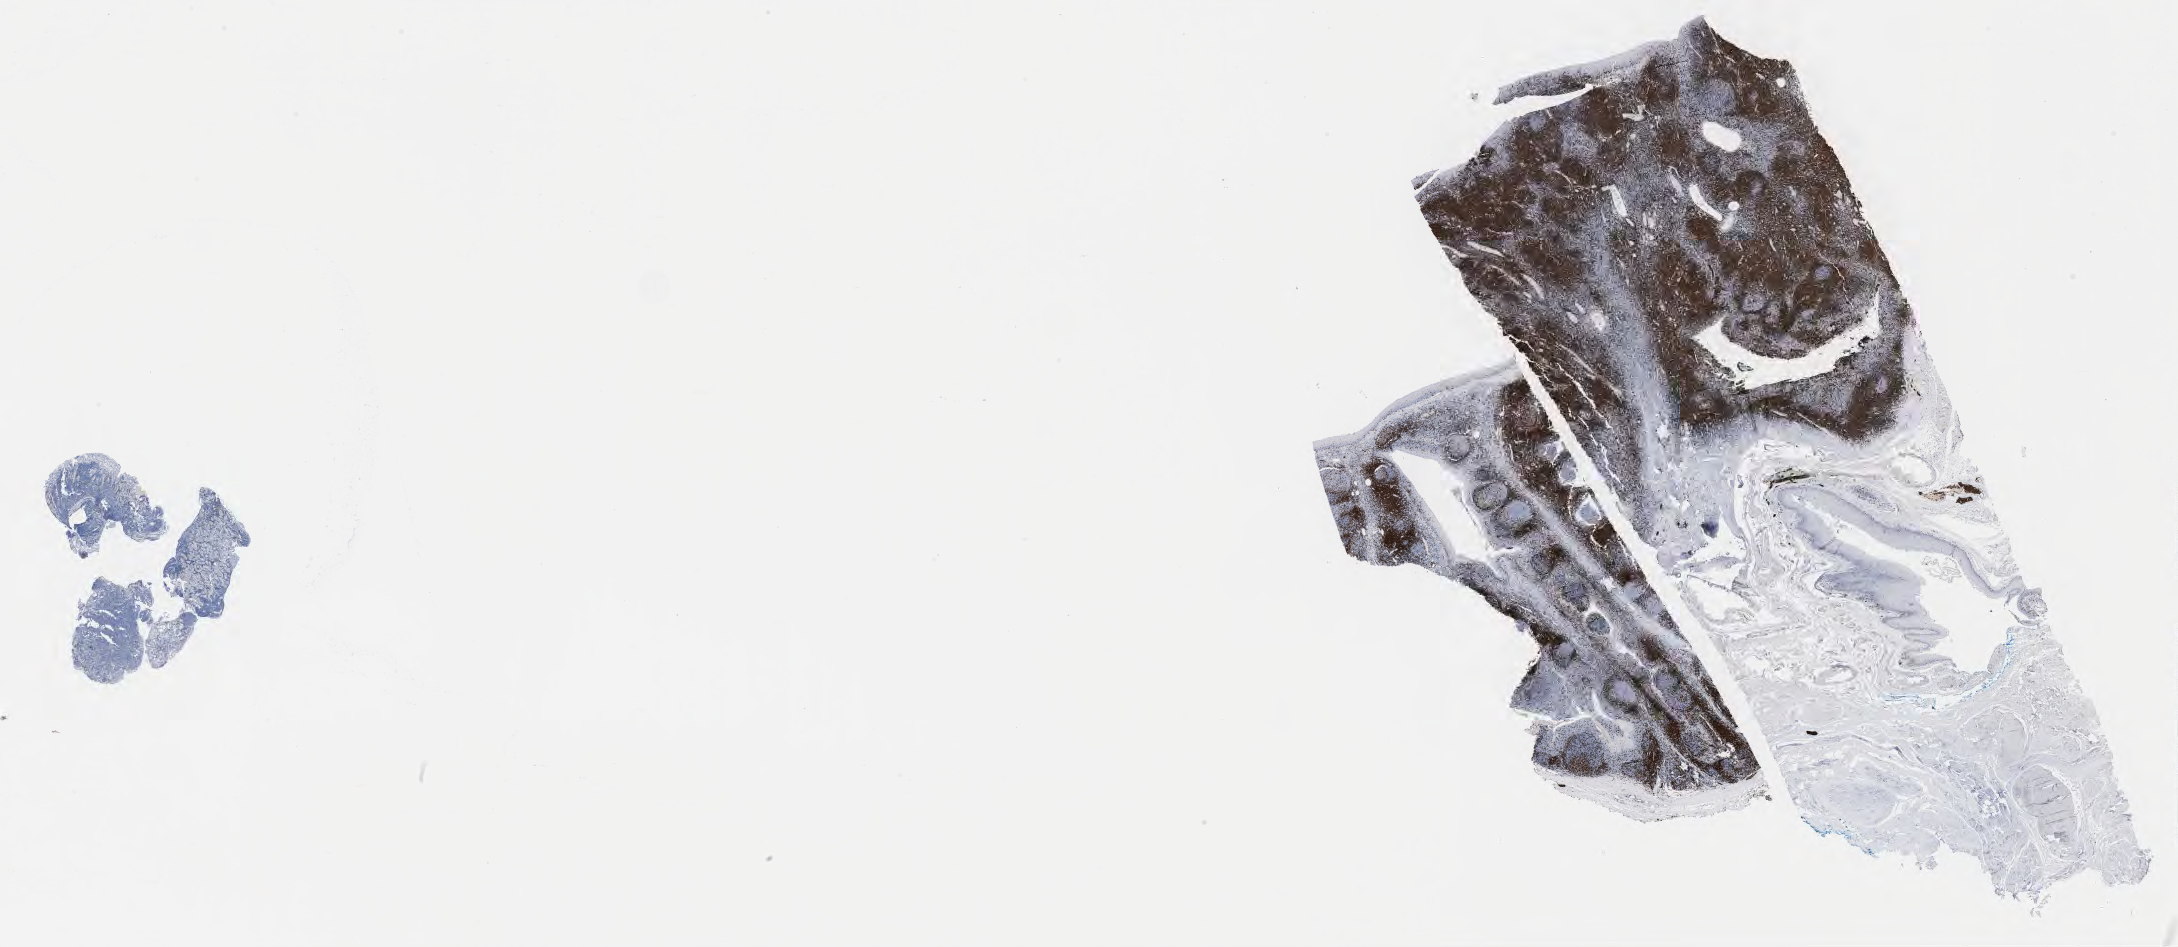
Whole-slide image, immunohistochemical stain for CD3, shown as a low-resolution overview of the whole scanned area (about 35.2 x 15.3 mm); tumor tissue. Patient: female, 45 years old.
Diagnosis: Burkitt lymphoma, NOS.